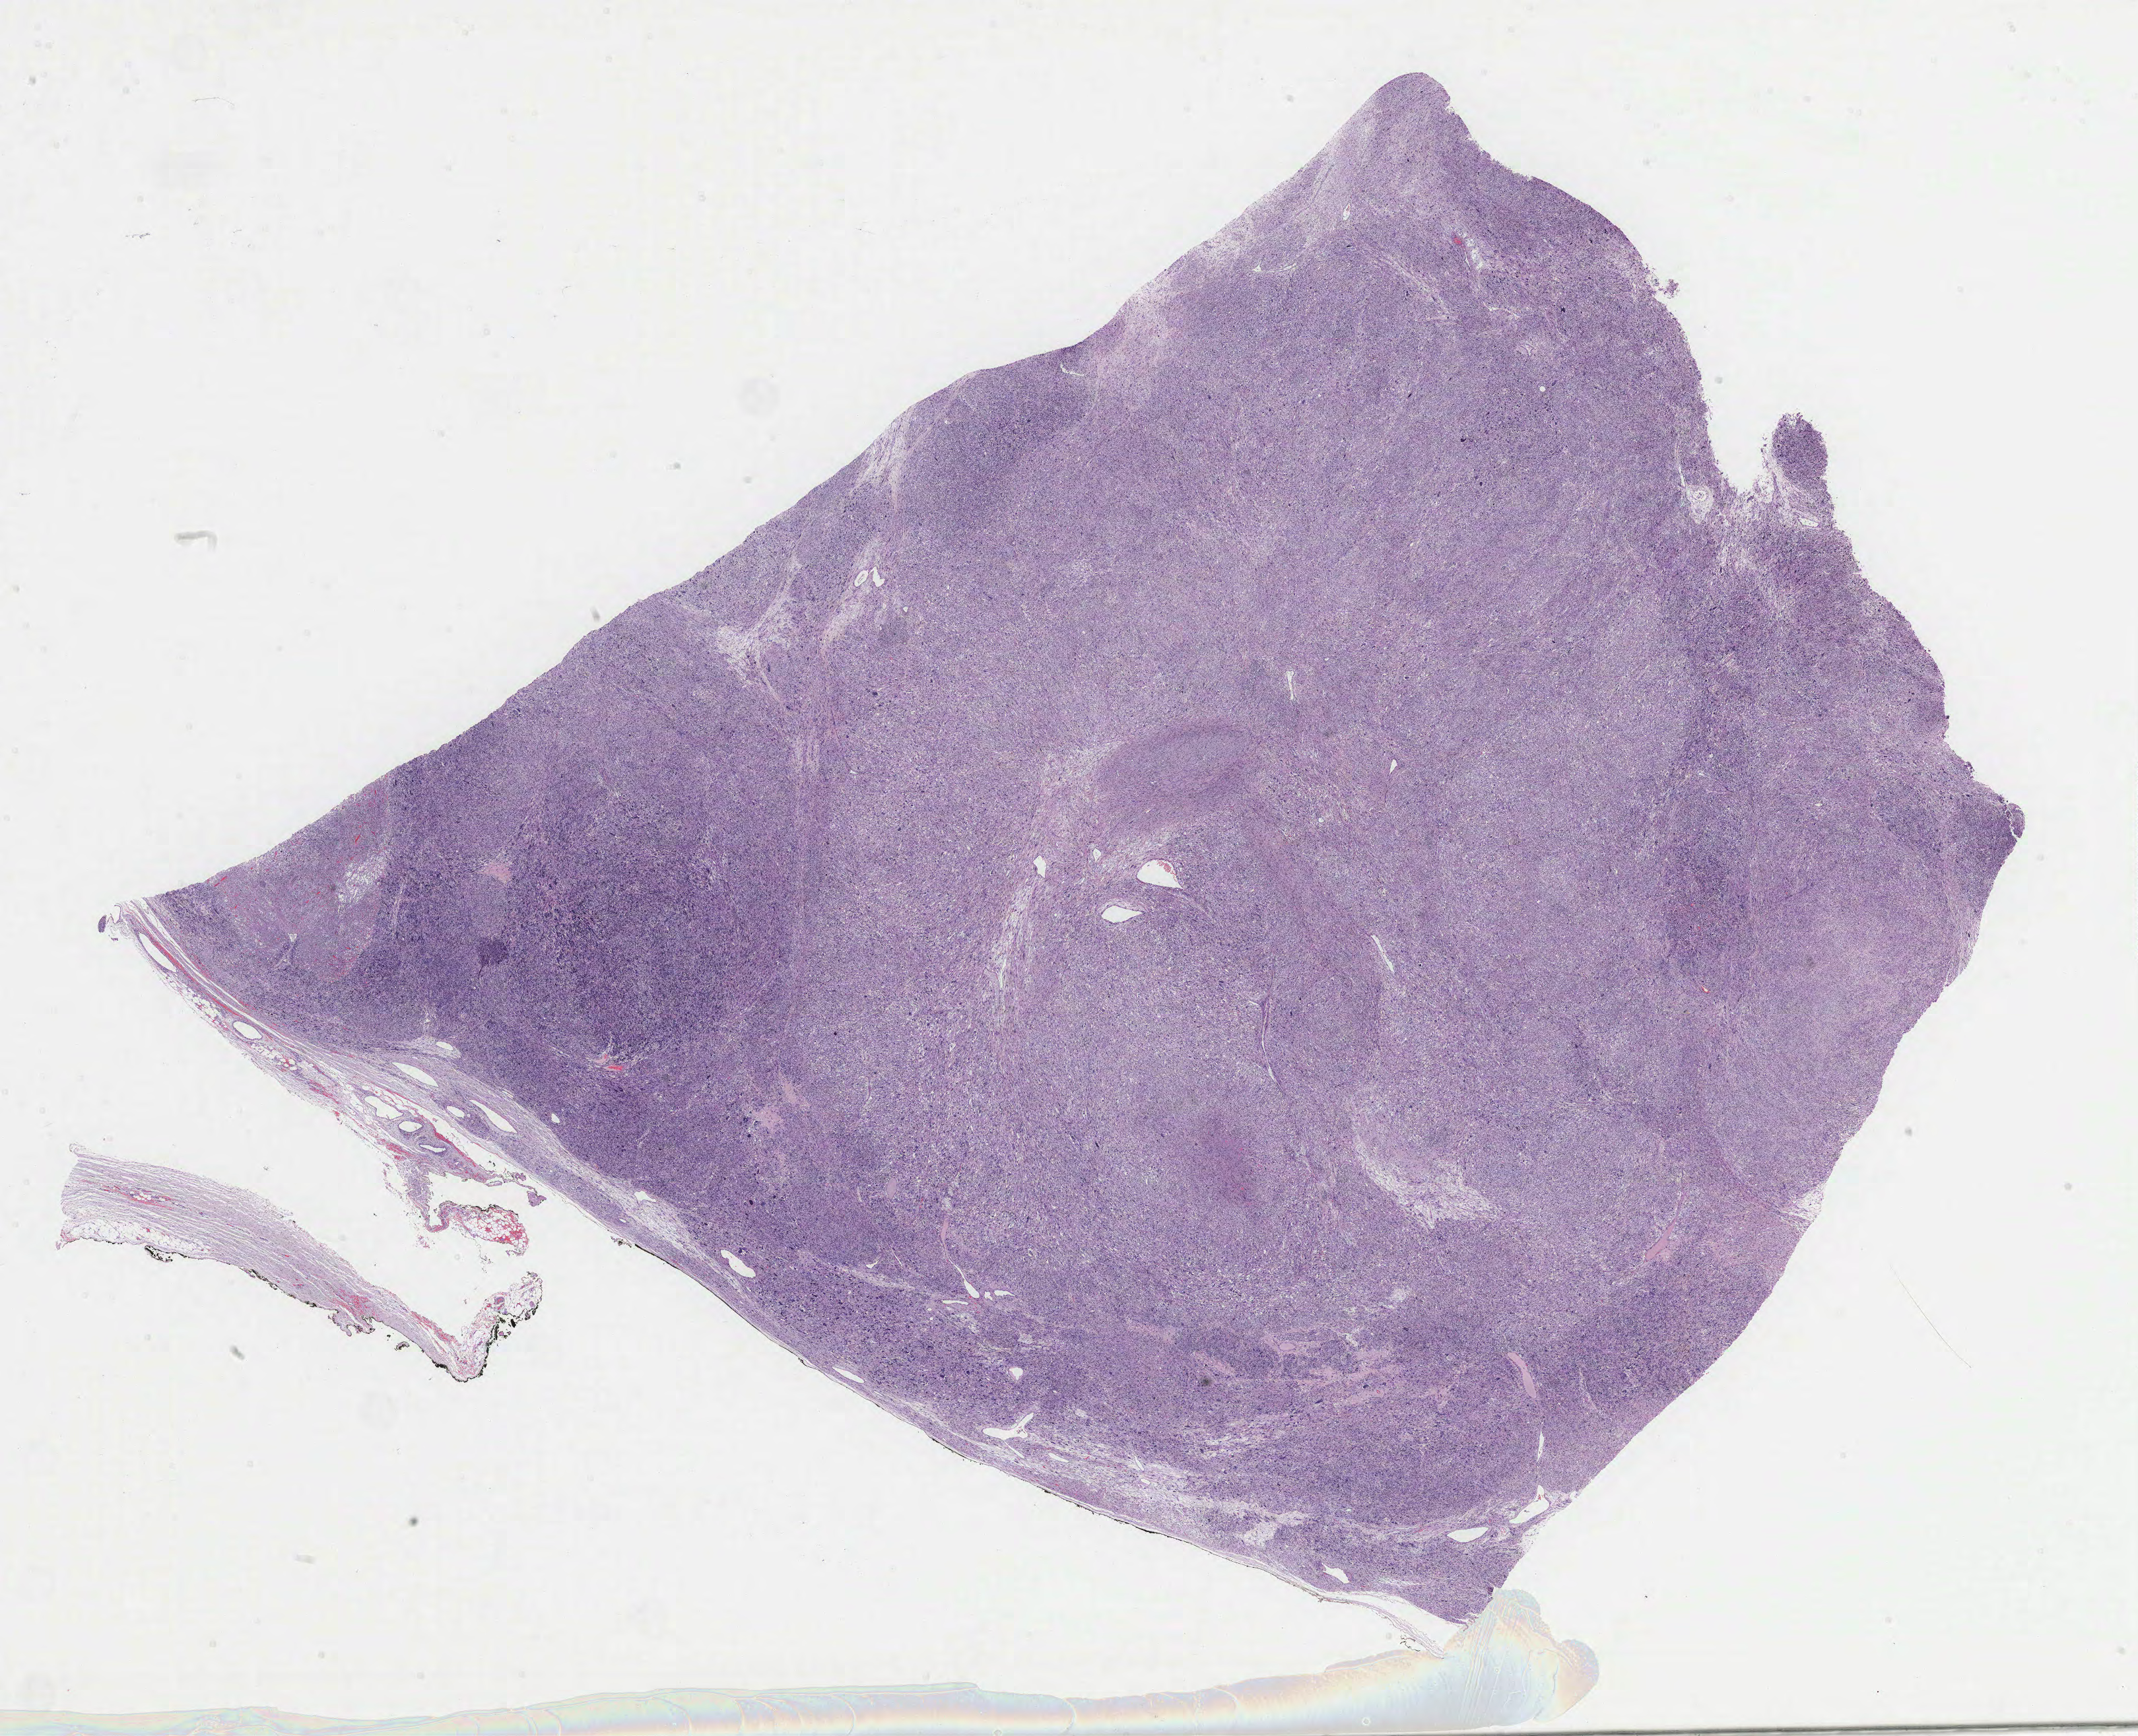
Whole-slide histology image, H&E-stained, low-resolution overview of the scanned area, about 26.2 x 21.2 mm (acquisition: 40x scan). Formalin-fixed paraffin-embedded (FFPE) diagnostic section. Primary tumour sample from the retroperitoneum and peritoneum. Female patient; age at initial diagnosis 57 years.
Histologic diagnosis: Leiomyosarcoma, NOS (retroperitoneum).